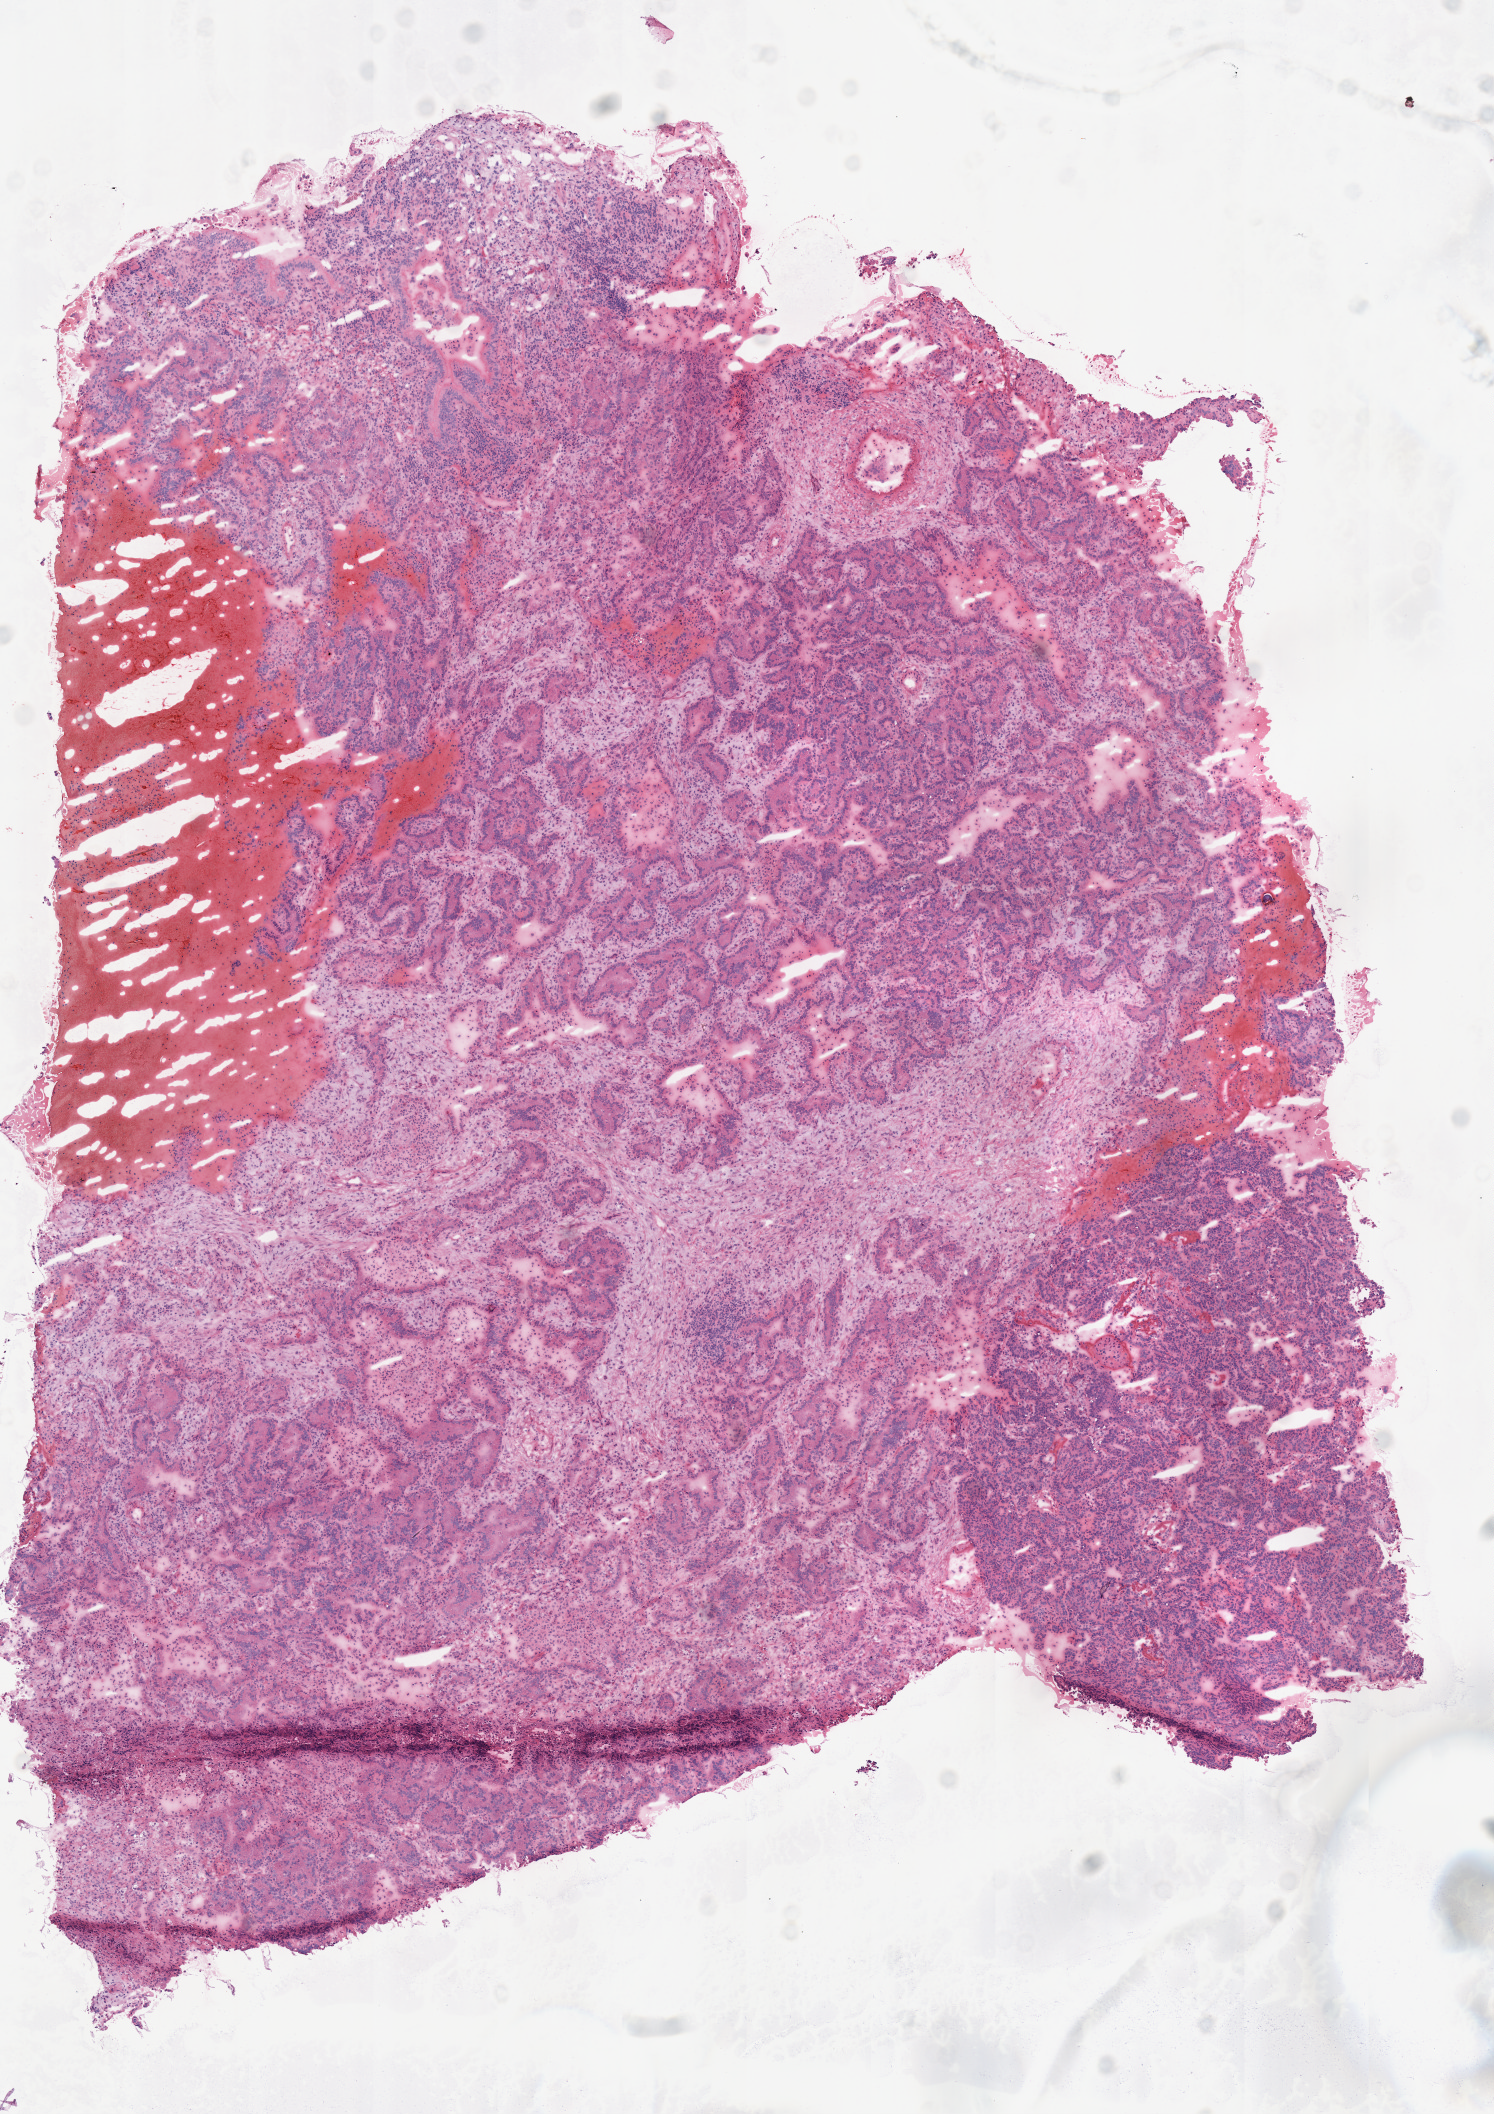
Whole-slide histology image, H&E — low-resolution overview of the scanned area, about 5.9 x 8.3 mm, frozen section from the top of the tissue portion, primary tumour sample from the lung. Patient: female, age at initial diagnosis 69 years. Composition of this section per pathologist review: tumour cells 100%, tumour nuclei 75%, normal cells 0%, stromal cells 0%, necrosis 0%. Inflammatory infiltration, as recorded: lymphocyte infiltration 10%, monocyte infiltration 5%, neutrophil infiltration 0%.
AJCC pathologic stage: IIB (7th edition). Diagnosis: Adenocarcinoma with mixed subtypes (lower lobe, lung).